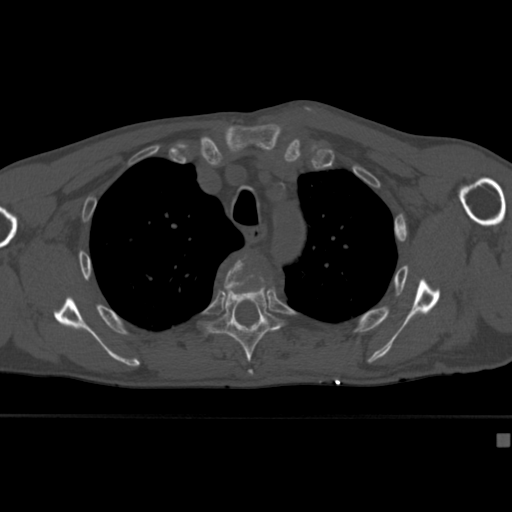
CT including the spine, one axial slice; position 312 of 430 along the scan axis; 120 kVp; bone window (W 1800 / L 400 HU); 512 × 512 image matrix, field of view 337 × 337 mm. Male patient, age 64 years. From the clinical record (not read from this slice): primary cancer: uterus; vertebrae with lytic lesions (as recorded): T1, T4, T5, T7, L5.
Outlined on this slice (semi-automatic segmentation, software-assisted and operator-edited):
- T4 vertebra: bounding box (x1, y1, x2, y2) in pixels: (224, 256, 273, 290)
- T5 vertebra: (201, 284, 286, 376)